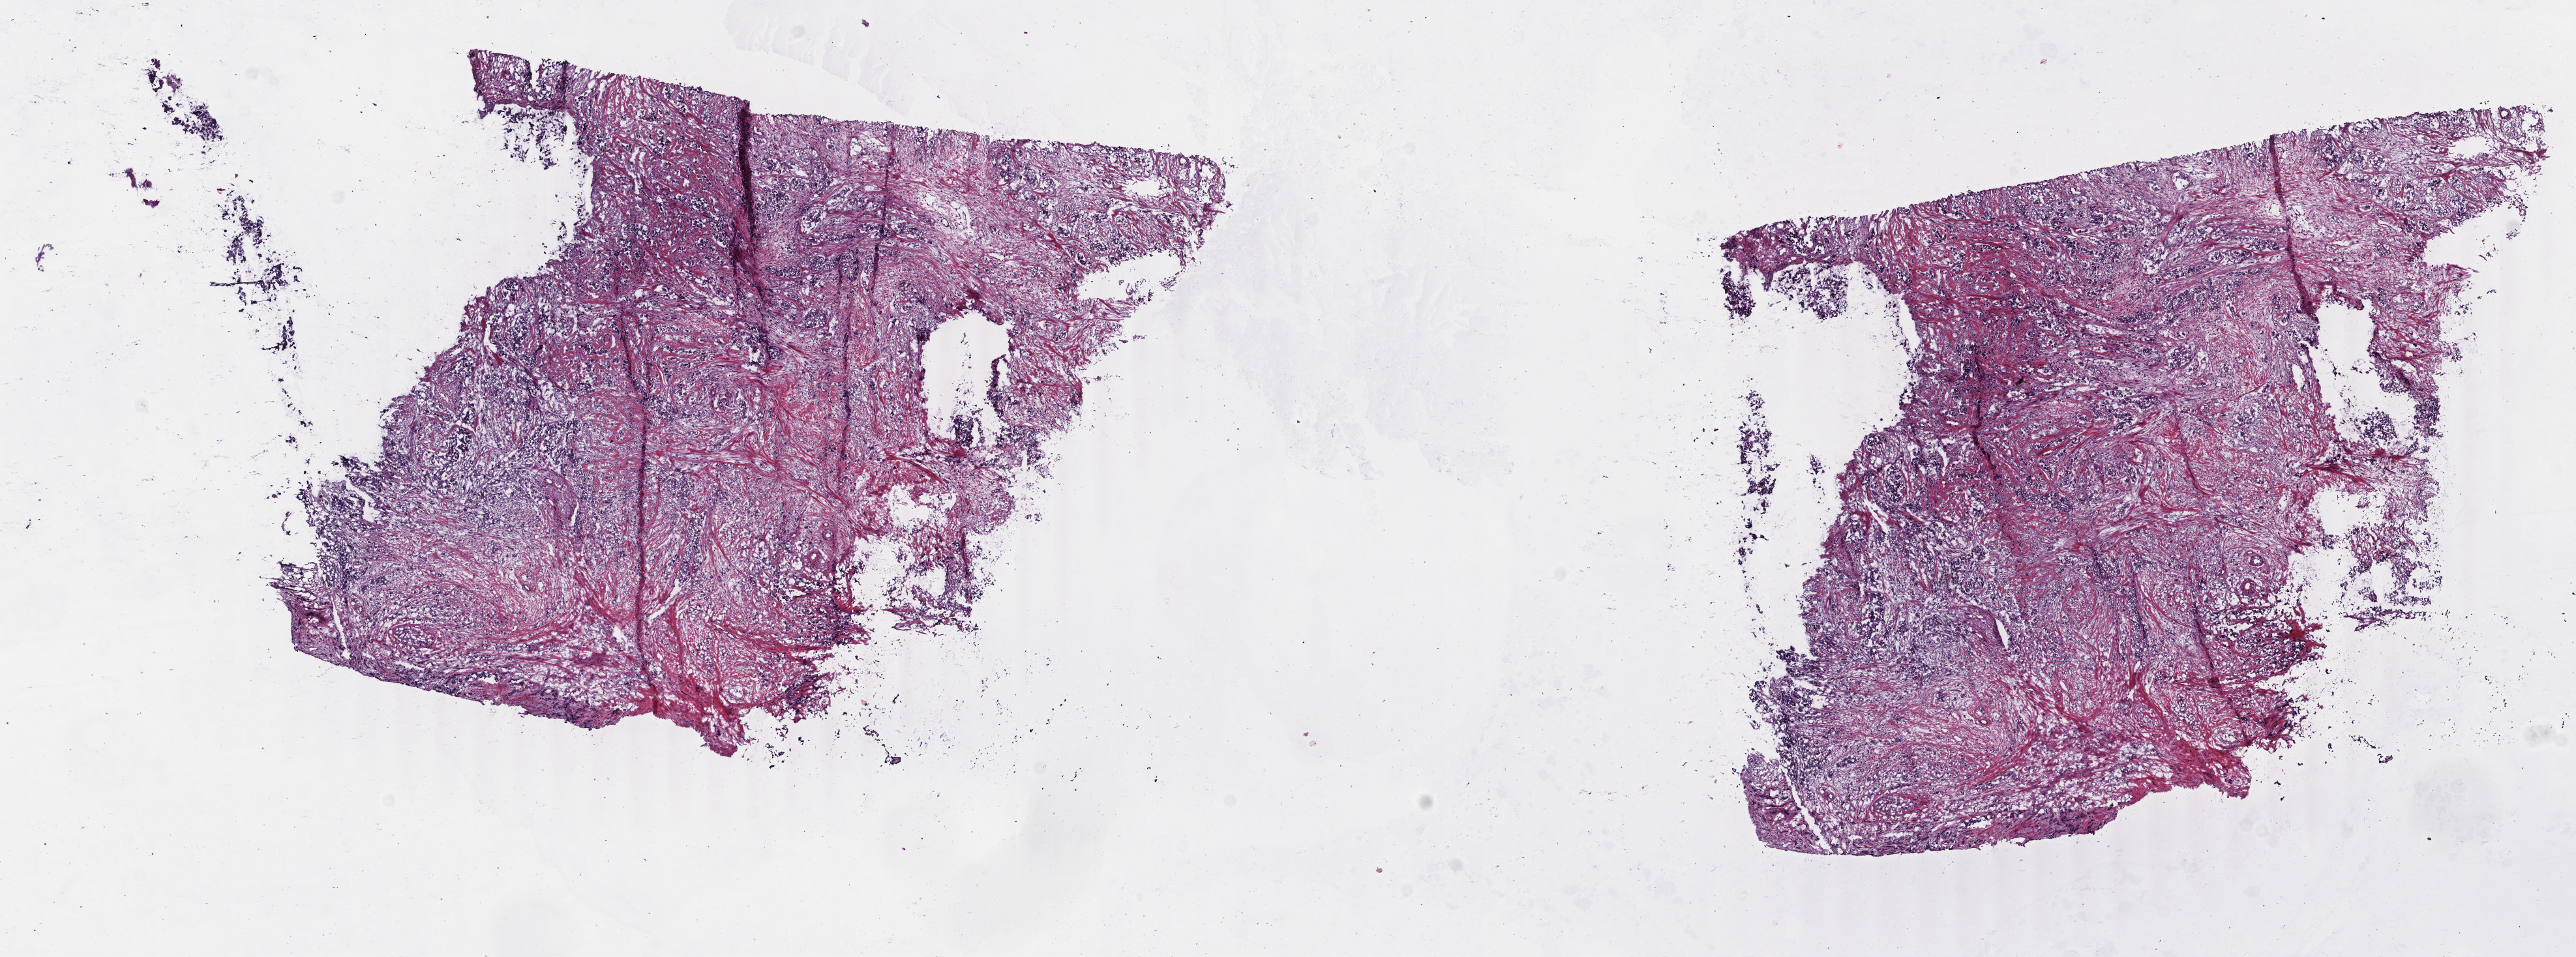
Hematoxylin and eosin (H&E) stained whole-slide image — shown as a low-resolution overview of the whole scanned area (about 15.7 x 5.8 mm, slide scanned at 40x), frozen section from the top of the tissue portion, sample: primary tumour, breast. Patient: female, age at initial diagnosis 50 years. Slide review estimates, as recorded: tumour cells 80%, tumour nuclei 65%, normal cells 5%, stromal cells 14%, necrosis 1%. Inflammatory infiltration, as recorded: lymphocyte infiltration 1%, monocyte infiltration 0%, neutrophil infiltration 0%.
Histologic diagnosis: Apocrine adenocarcinoma. Lymph nodes positive (case pathology): 1 of 19 examined. AJCC pathologic stage: IIB (6th edition).